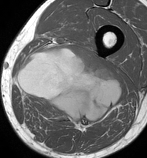
MRI of an extremity soft-tissue mass, one axial slice; slice 48 of 86 in the series (ordered by position); MR volume resampled by the dataset authors to the PET/CT grid (not the native acquisition matrix); 147 × 158 image matrix. Male patient. Case-level facts recorded for this patient, not image findings: histological type: undifferentiated pleomorphic liposarcoma; grade: high; site of the primary tumour: left thigh.
Outlined on this slice (expert contour drawn on MRI and transferred to this co-registered scan by the dataset authors):
- gross tumour volume including surrounding oedema: bounding box (x1, y1, x2, y2) in pixels: (14, 44, 122, 130)
- gross tumour volume (mass): (16, 44, 122, 130)